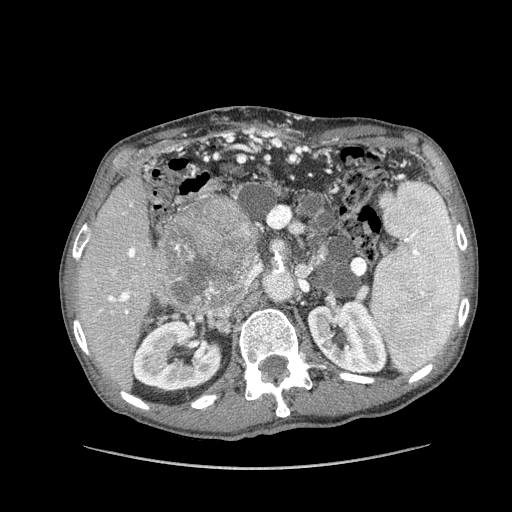
Contrast-enhanced abdominal CT (liver protocol), one axial slice. Position 63 of 162 along the scan axis. 100 kVp. Soft-tissue window (W 400 / L 40 HU). 2.5 mm slice thickness. 512 × 512 image matrix. From the clinical record (not read from this slice): diagnosis: hepatocellular carcinoma (patient treated with transarterial chemoembolisation; whether this scan precedes or follows treatment is not stated here); TNM stage (as recorded): Stage-IIIA; Child-Pugh class: A; tumour nodularity: multinodular; tumour size: 9.9 cm.
Structures marked on this image (semi-automatically segmented with operator editing):
- liver parenchyma outside the tumour (the mass and vessels are separate outlines, so this box may not span the whole liver): bounding box <78,168,191,386> (left, top, right, bottom; pixels)
- mass: <156,197,262,312>
- liver vessels: <99,203,145,342>